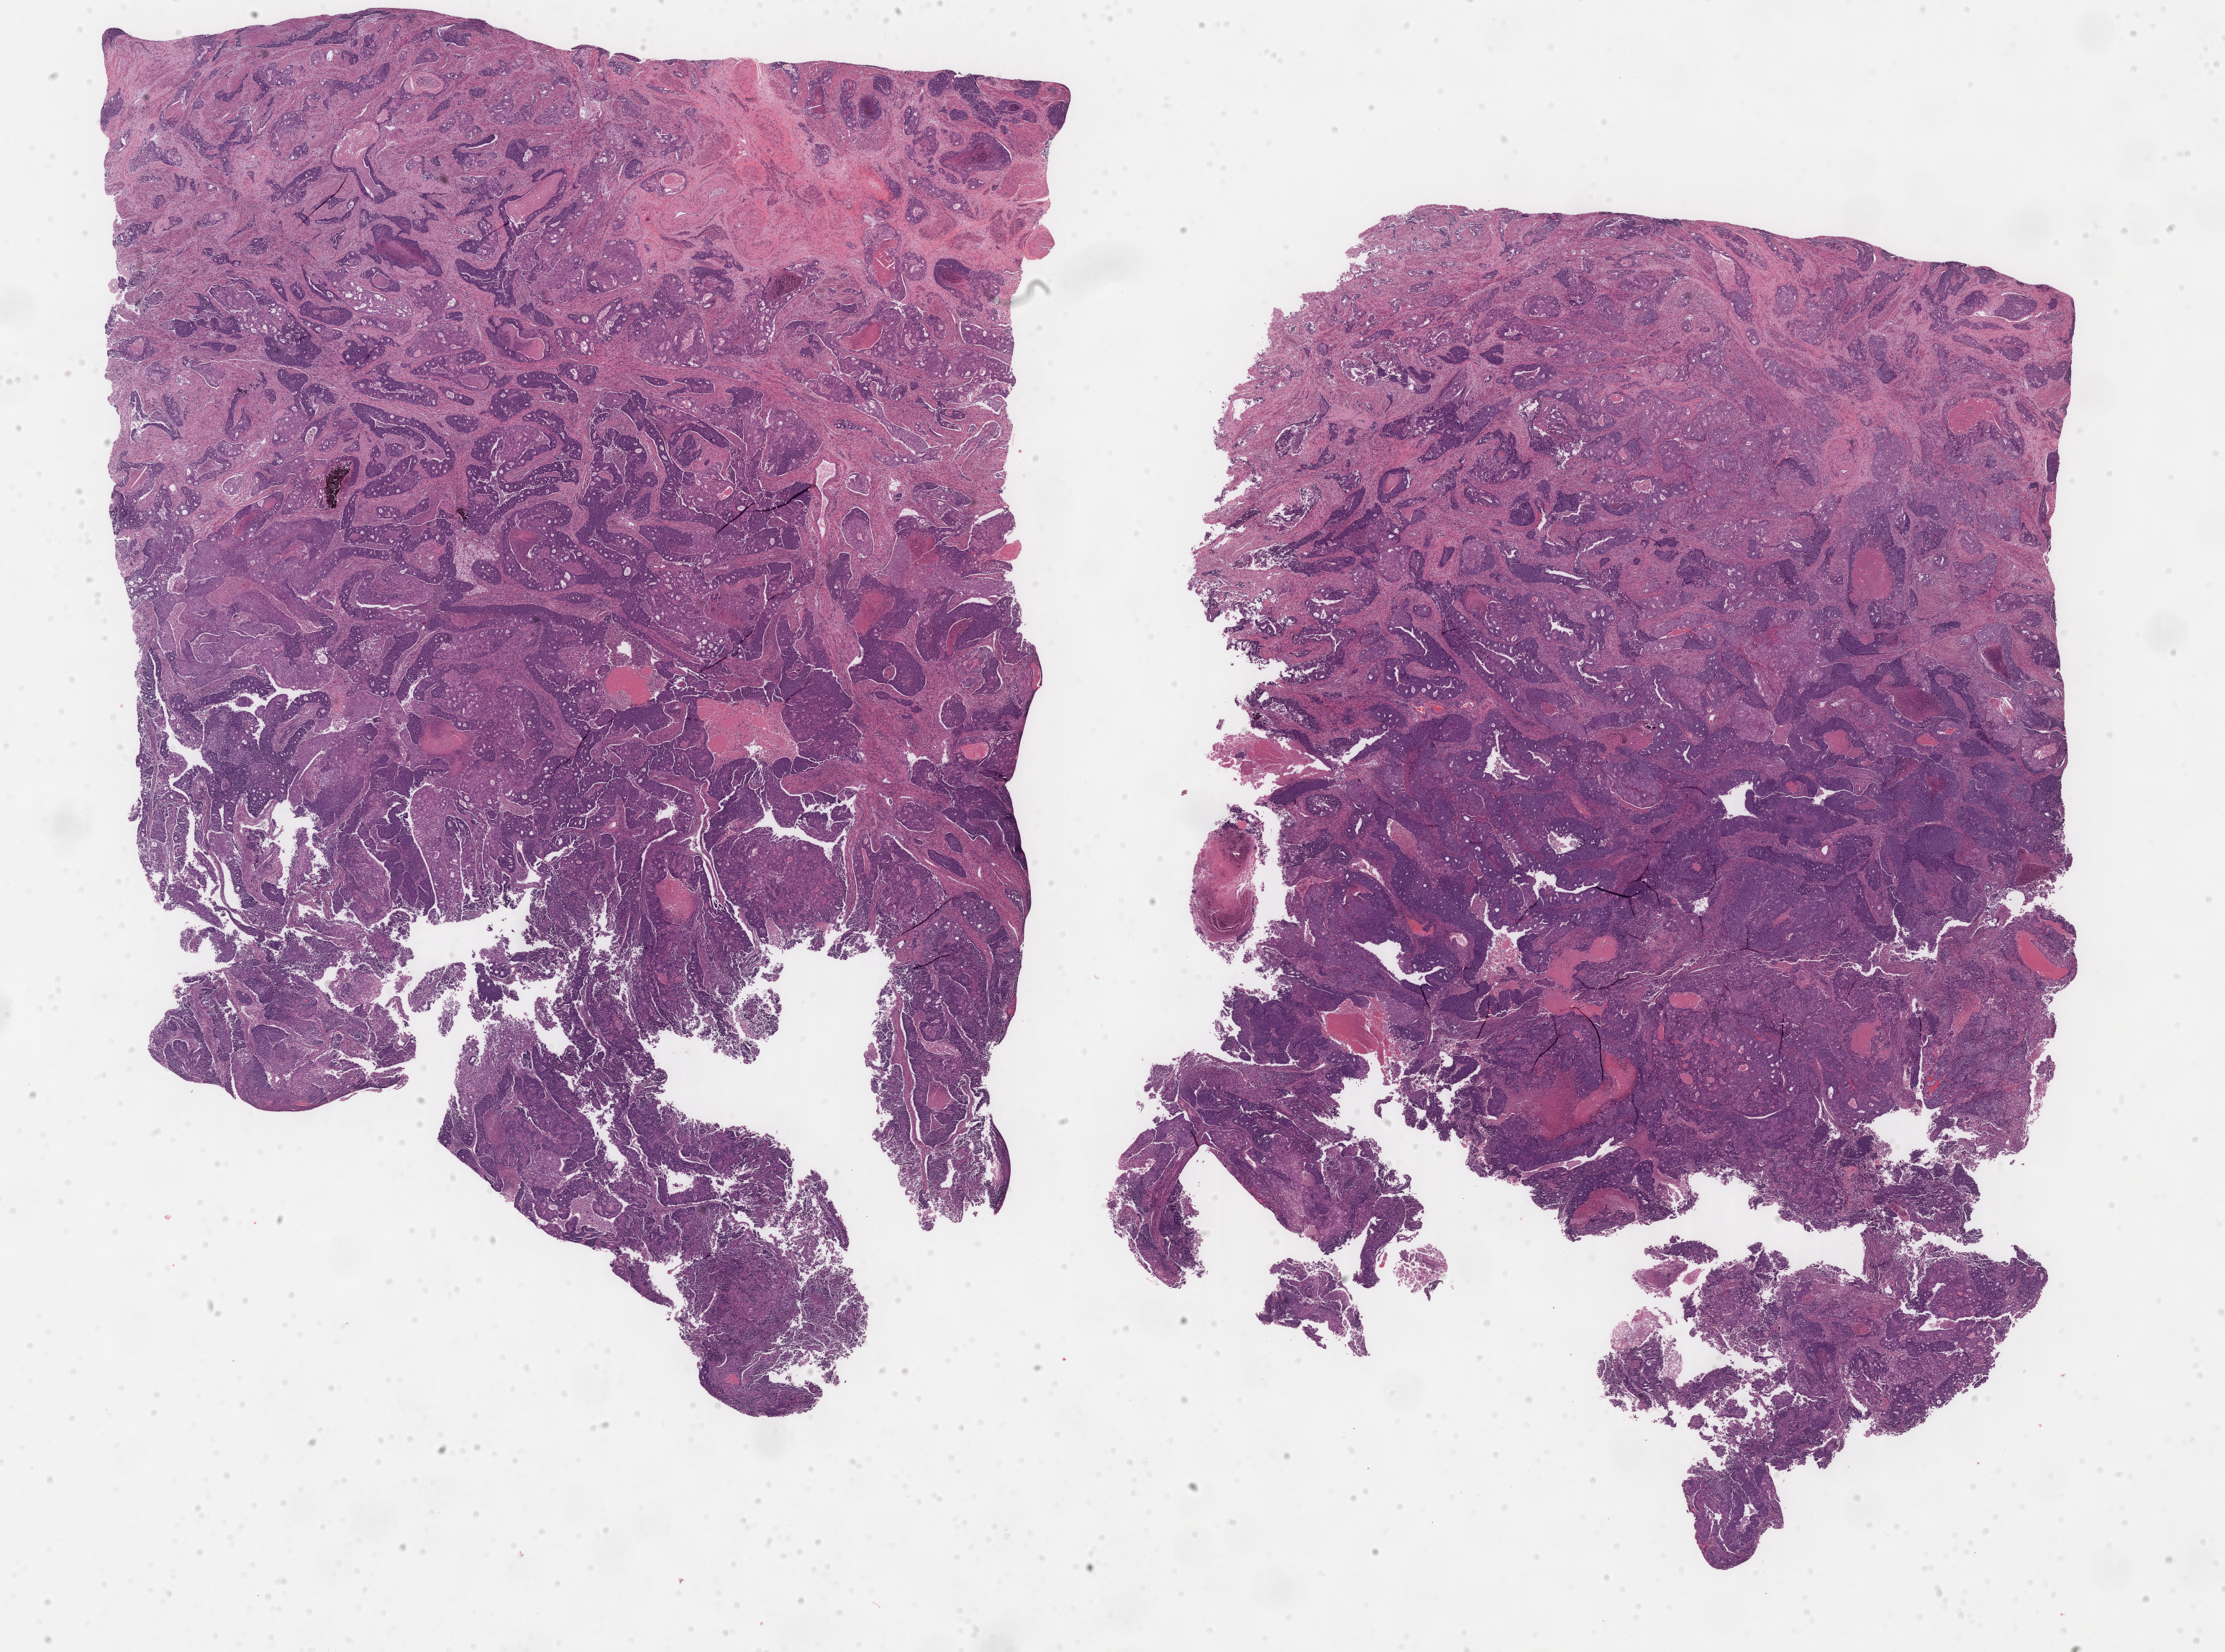
Whole-slide histology image, H&E — a low-resolution overview of the entire scanned area, about 24.6 x 18.2 mm (from a 40x scan); formalin-fixed paraffin-embedded (FFPE) diagnostic section; sample: primary tumour, uterus. Female patient; age at initial diagnosis 53 years. Histologic grade: G3 (poorly differentiated).
FIGO stage: IIIC. Histologic diagnosis: Endometrioid adenocarcinoma, NOS (endometrium).